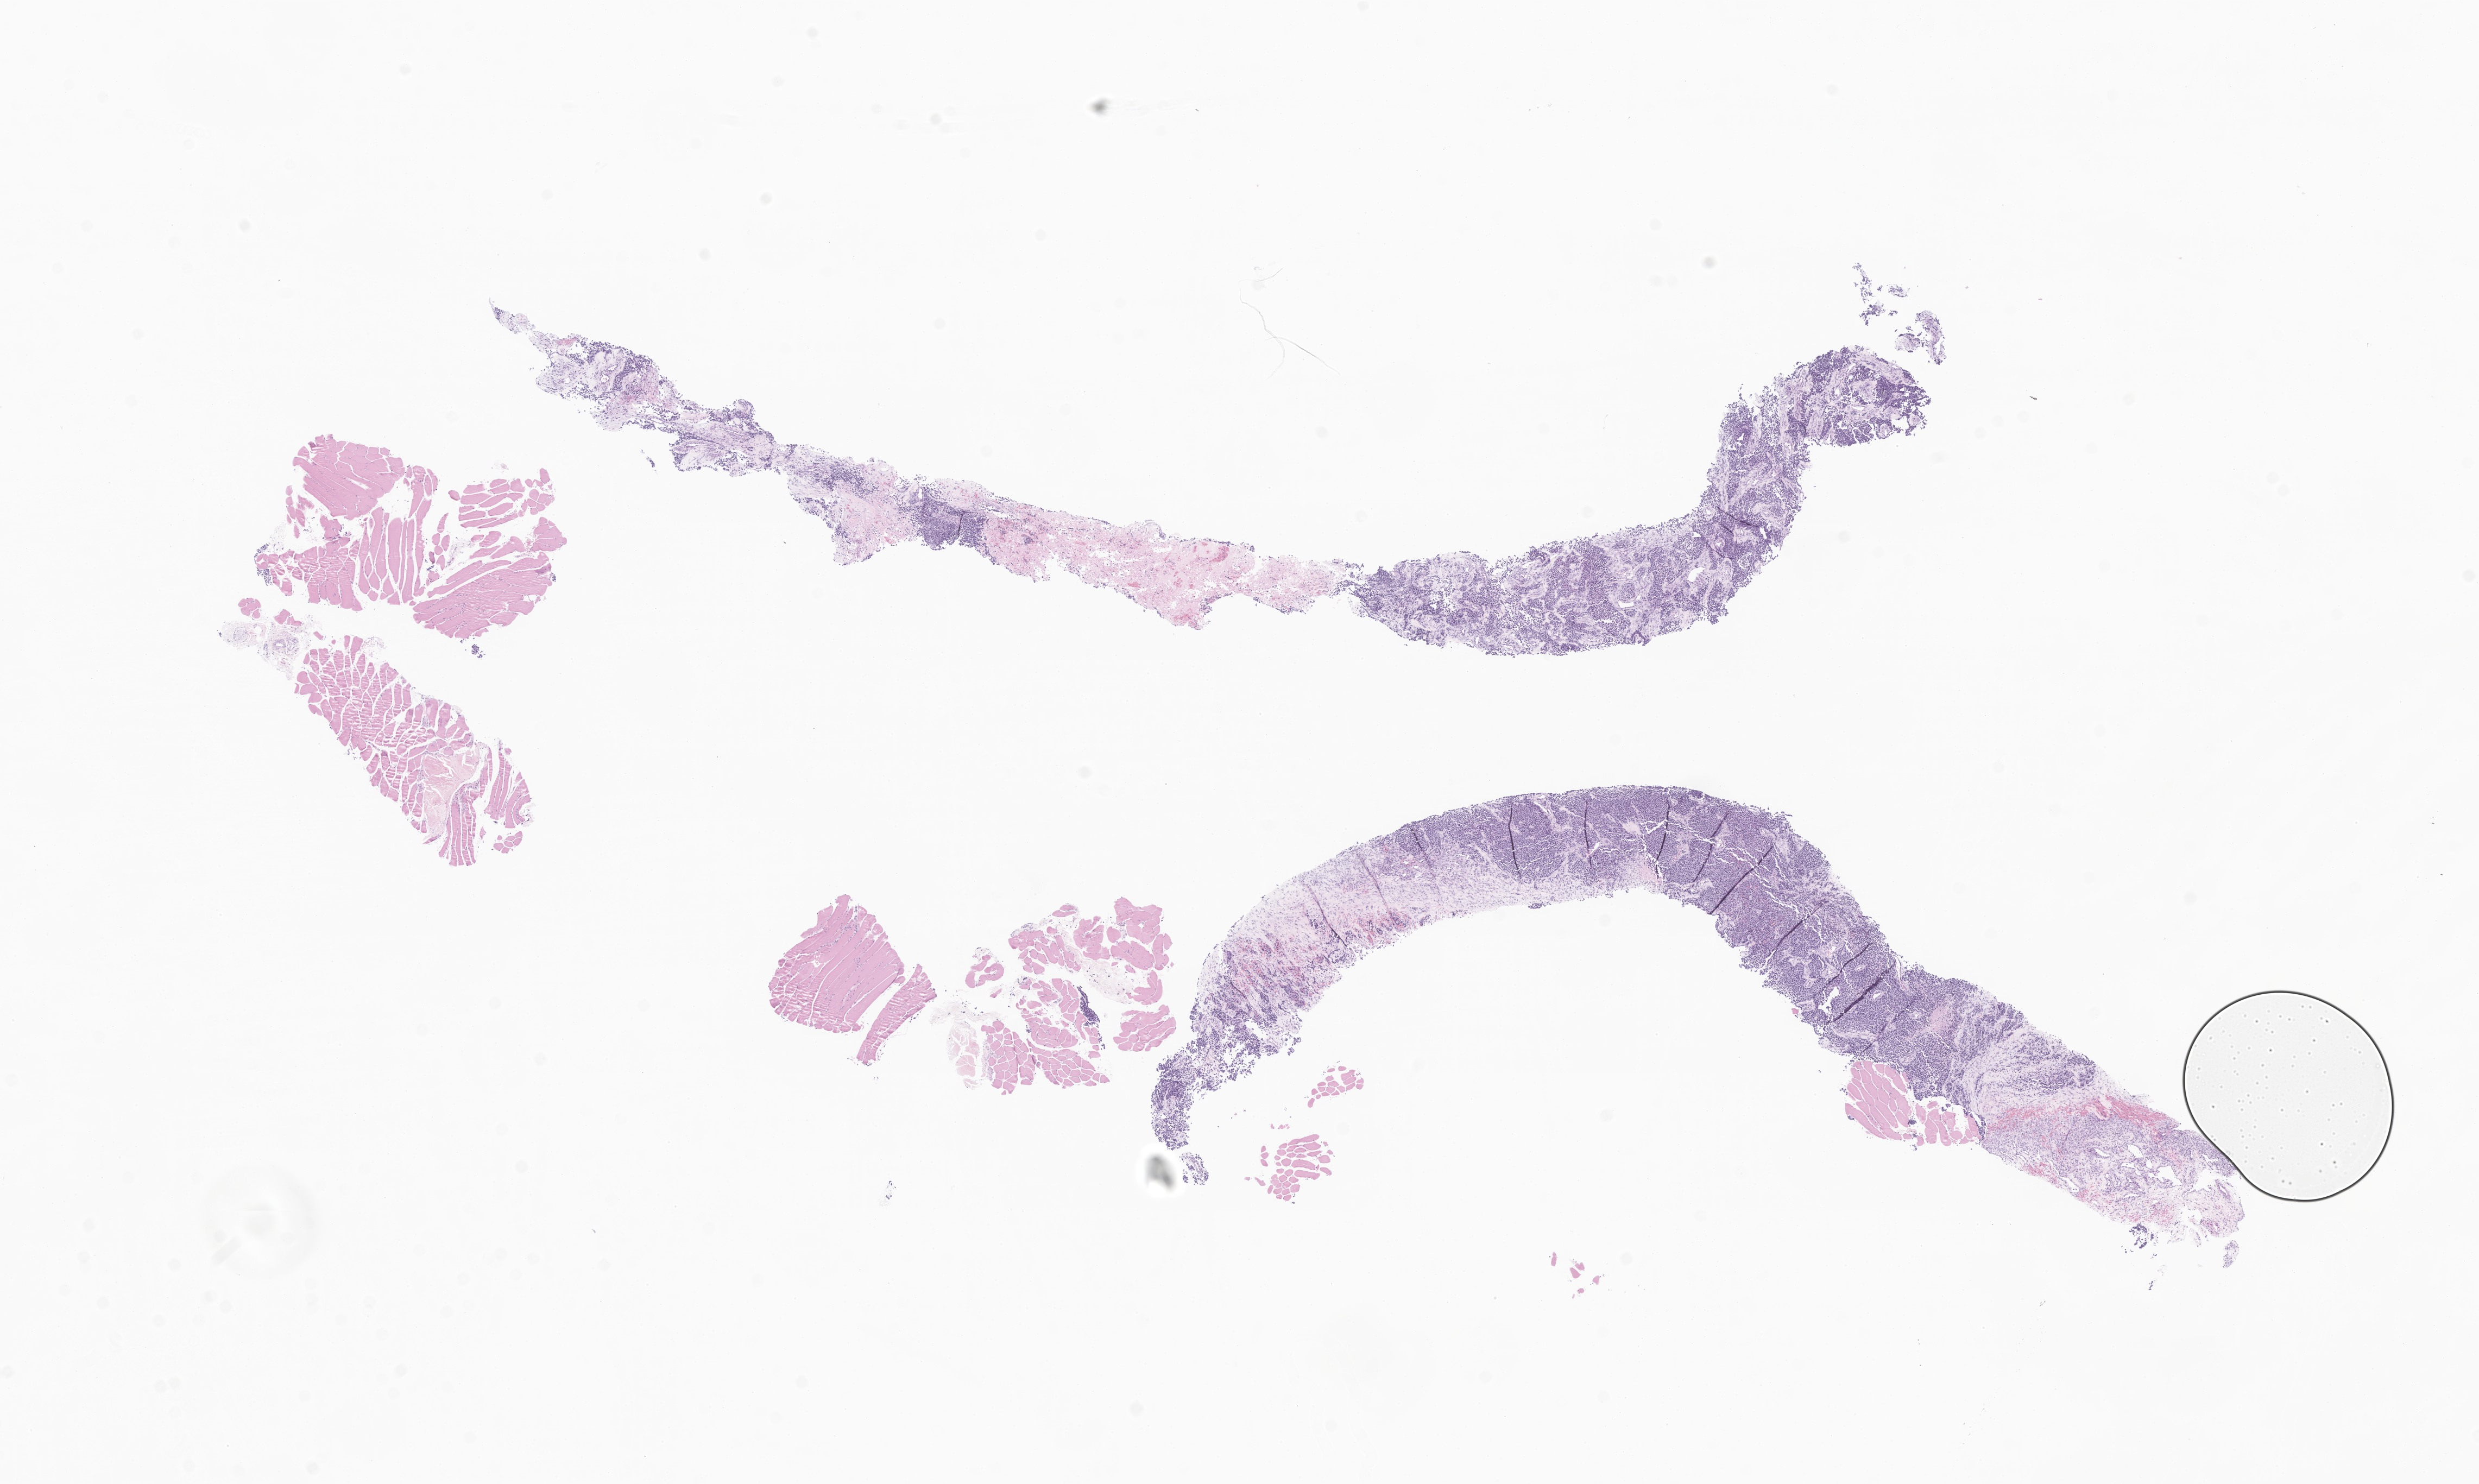
Whole-slide image, haematoxylin and eosin stain of tumor tissue from the upper limb lymph node, whole scanned area (about 19.2 x 11.5 mm) shown as a low-resolution overview. Formalin-fixed, paraffin-embedded (FFPE) tissue. Male patient, age 226 months (18 years 10 months).
Recorded diagnosis: Rhabdomyosarcoma, NOS.